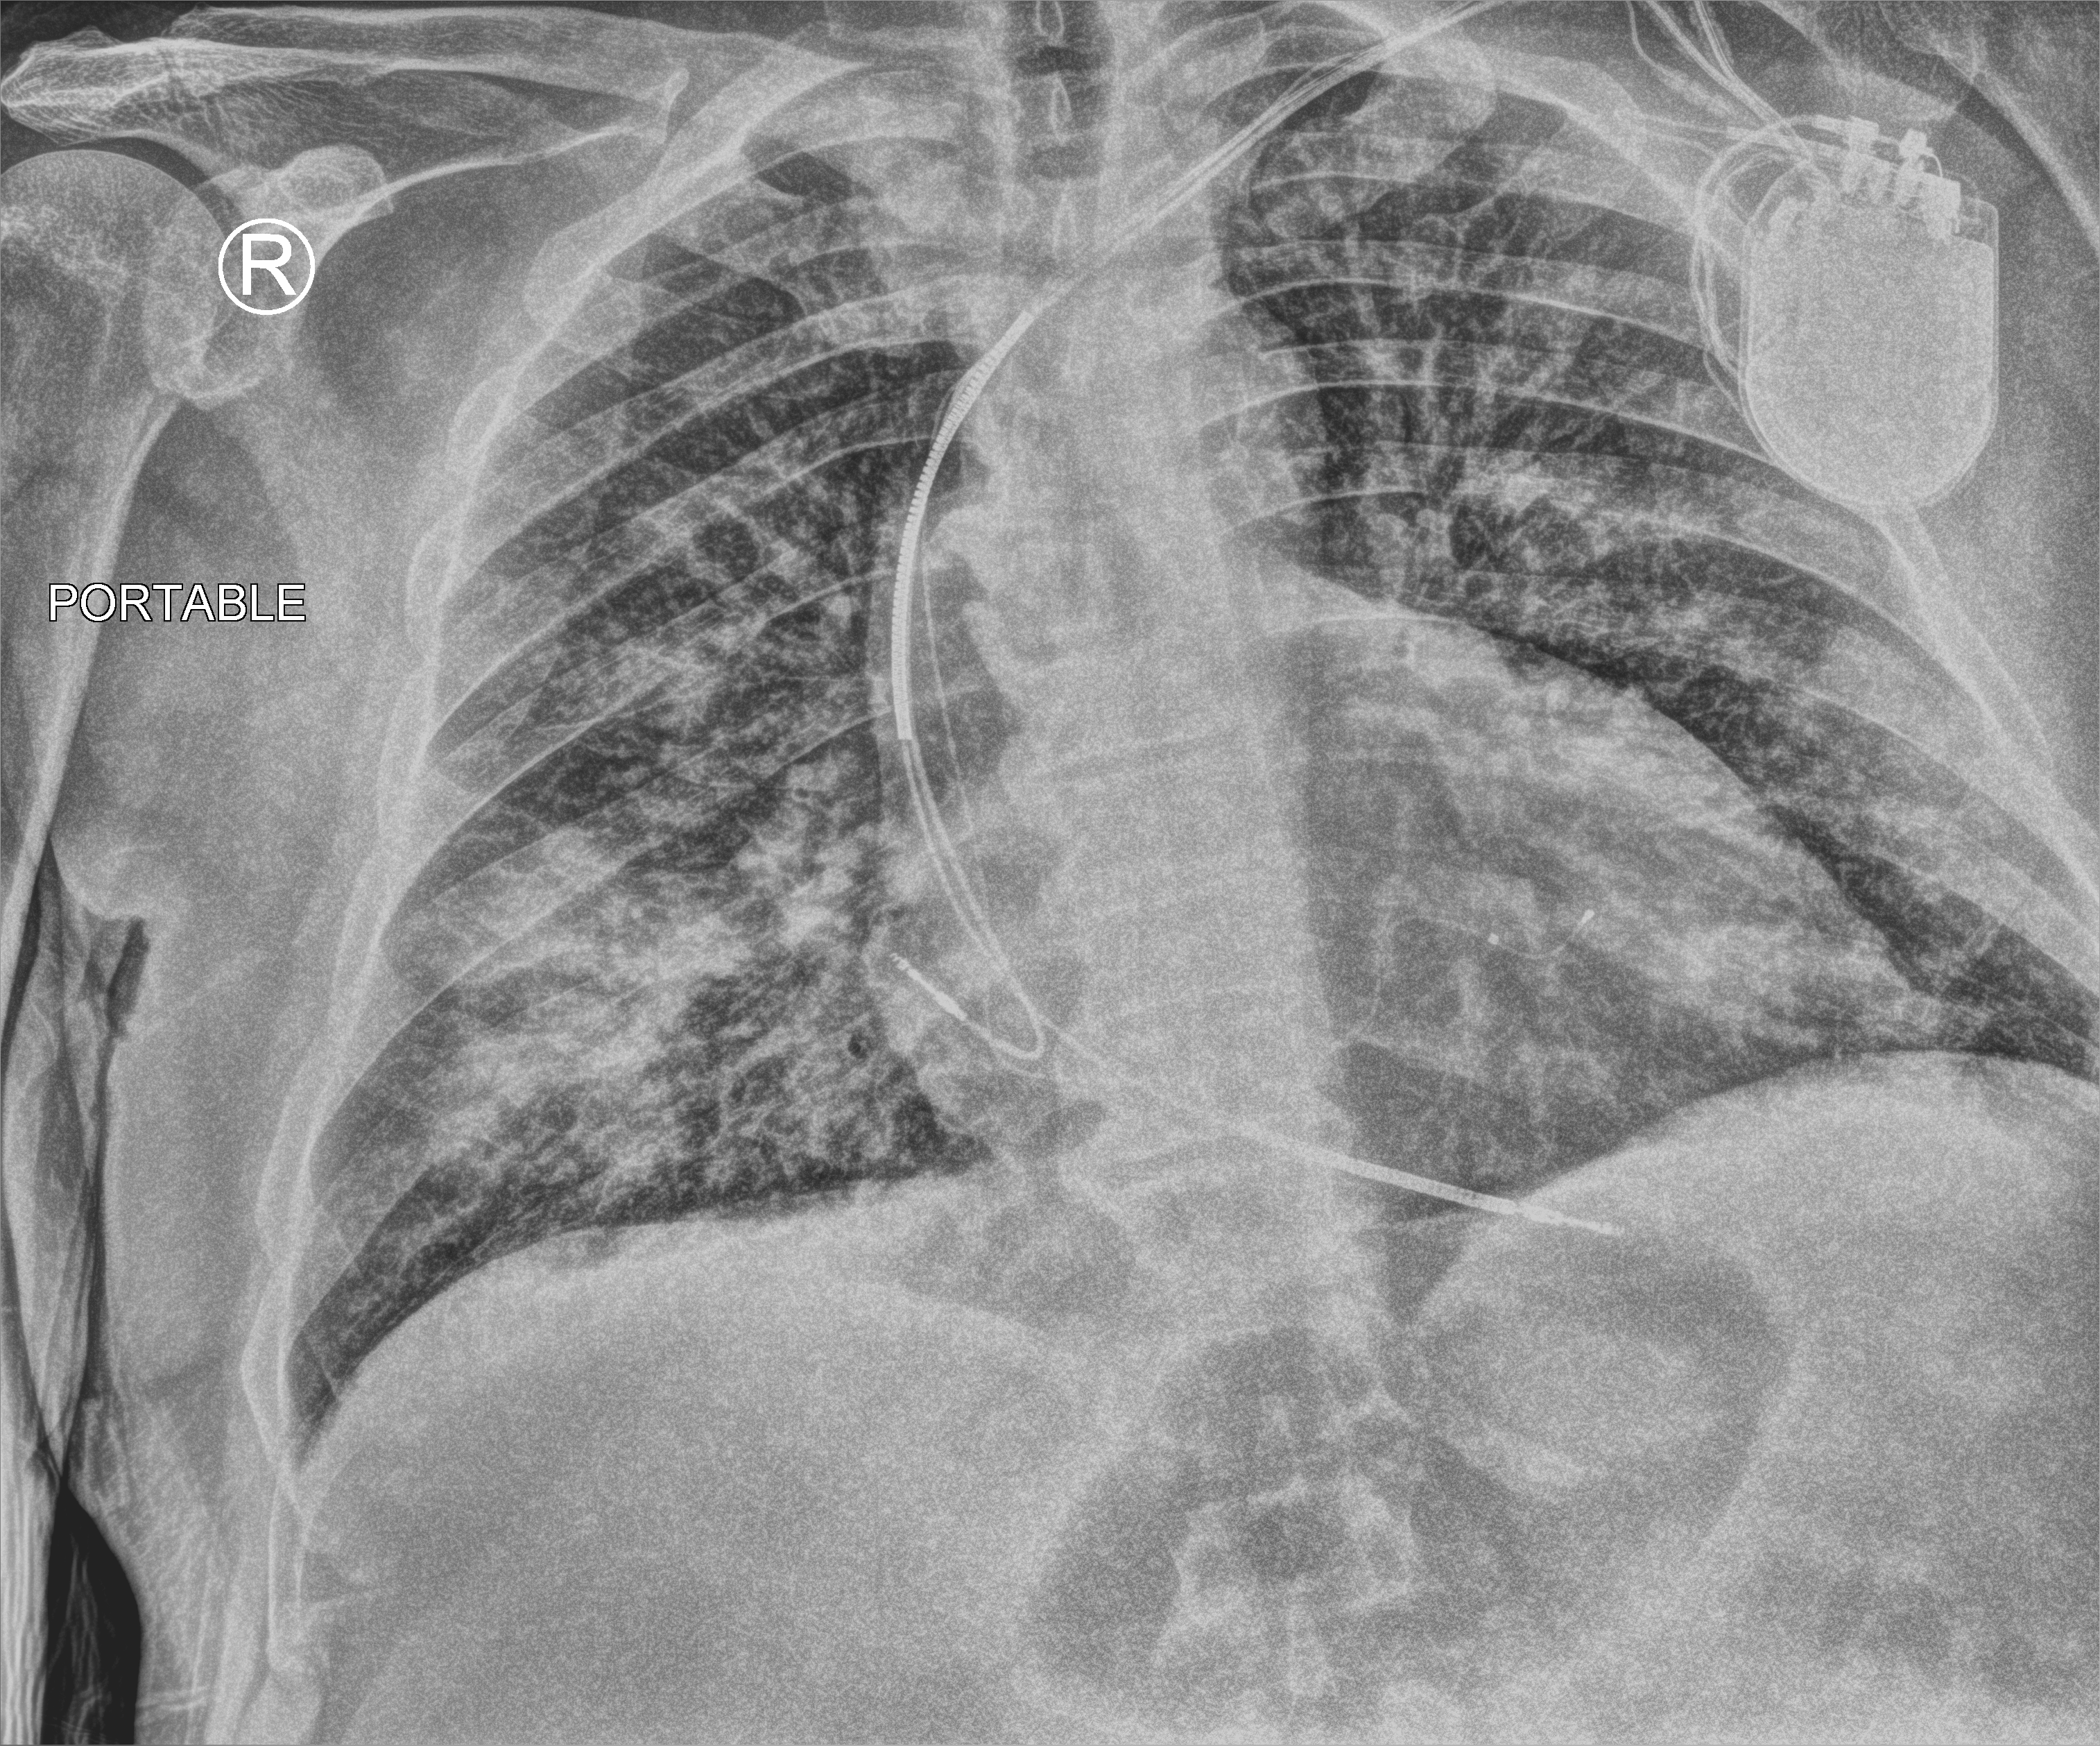
Chest X-ray (portable), anteroposterior (AP) projection. Patient hospitalised with COVID-19; male, aged 60–74 years.
From the hospital-stay record, not from the radiograph (when in the stay this image was taken is not recorded): admitted to intensive care during this hospital stay: no; mechanically ventilated during this hospital stay: no.